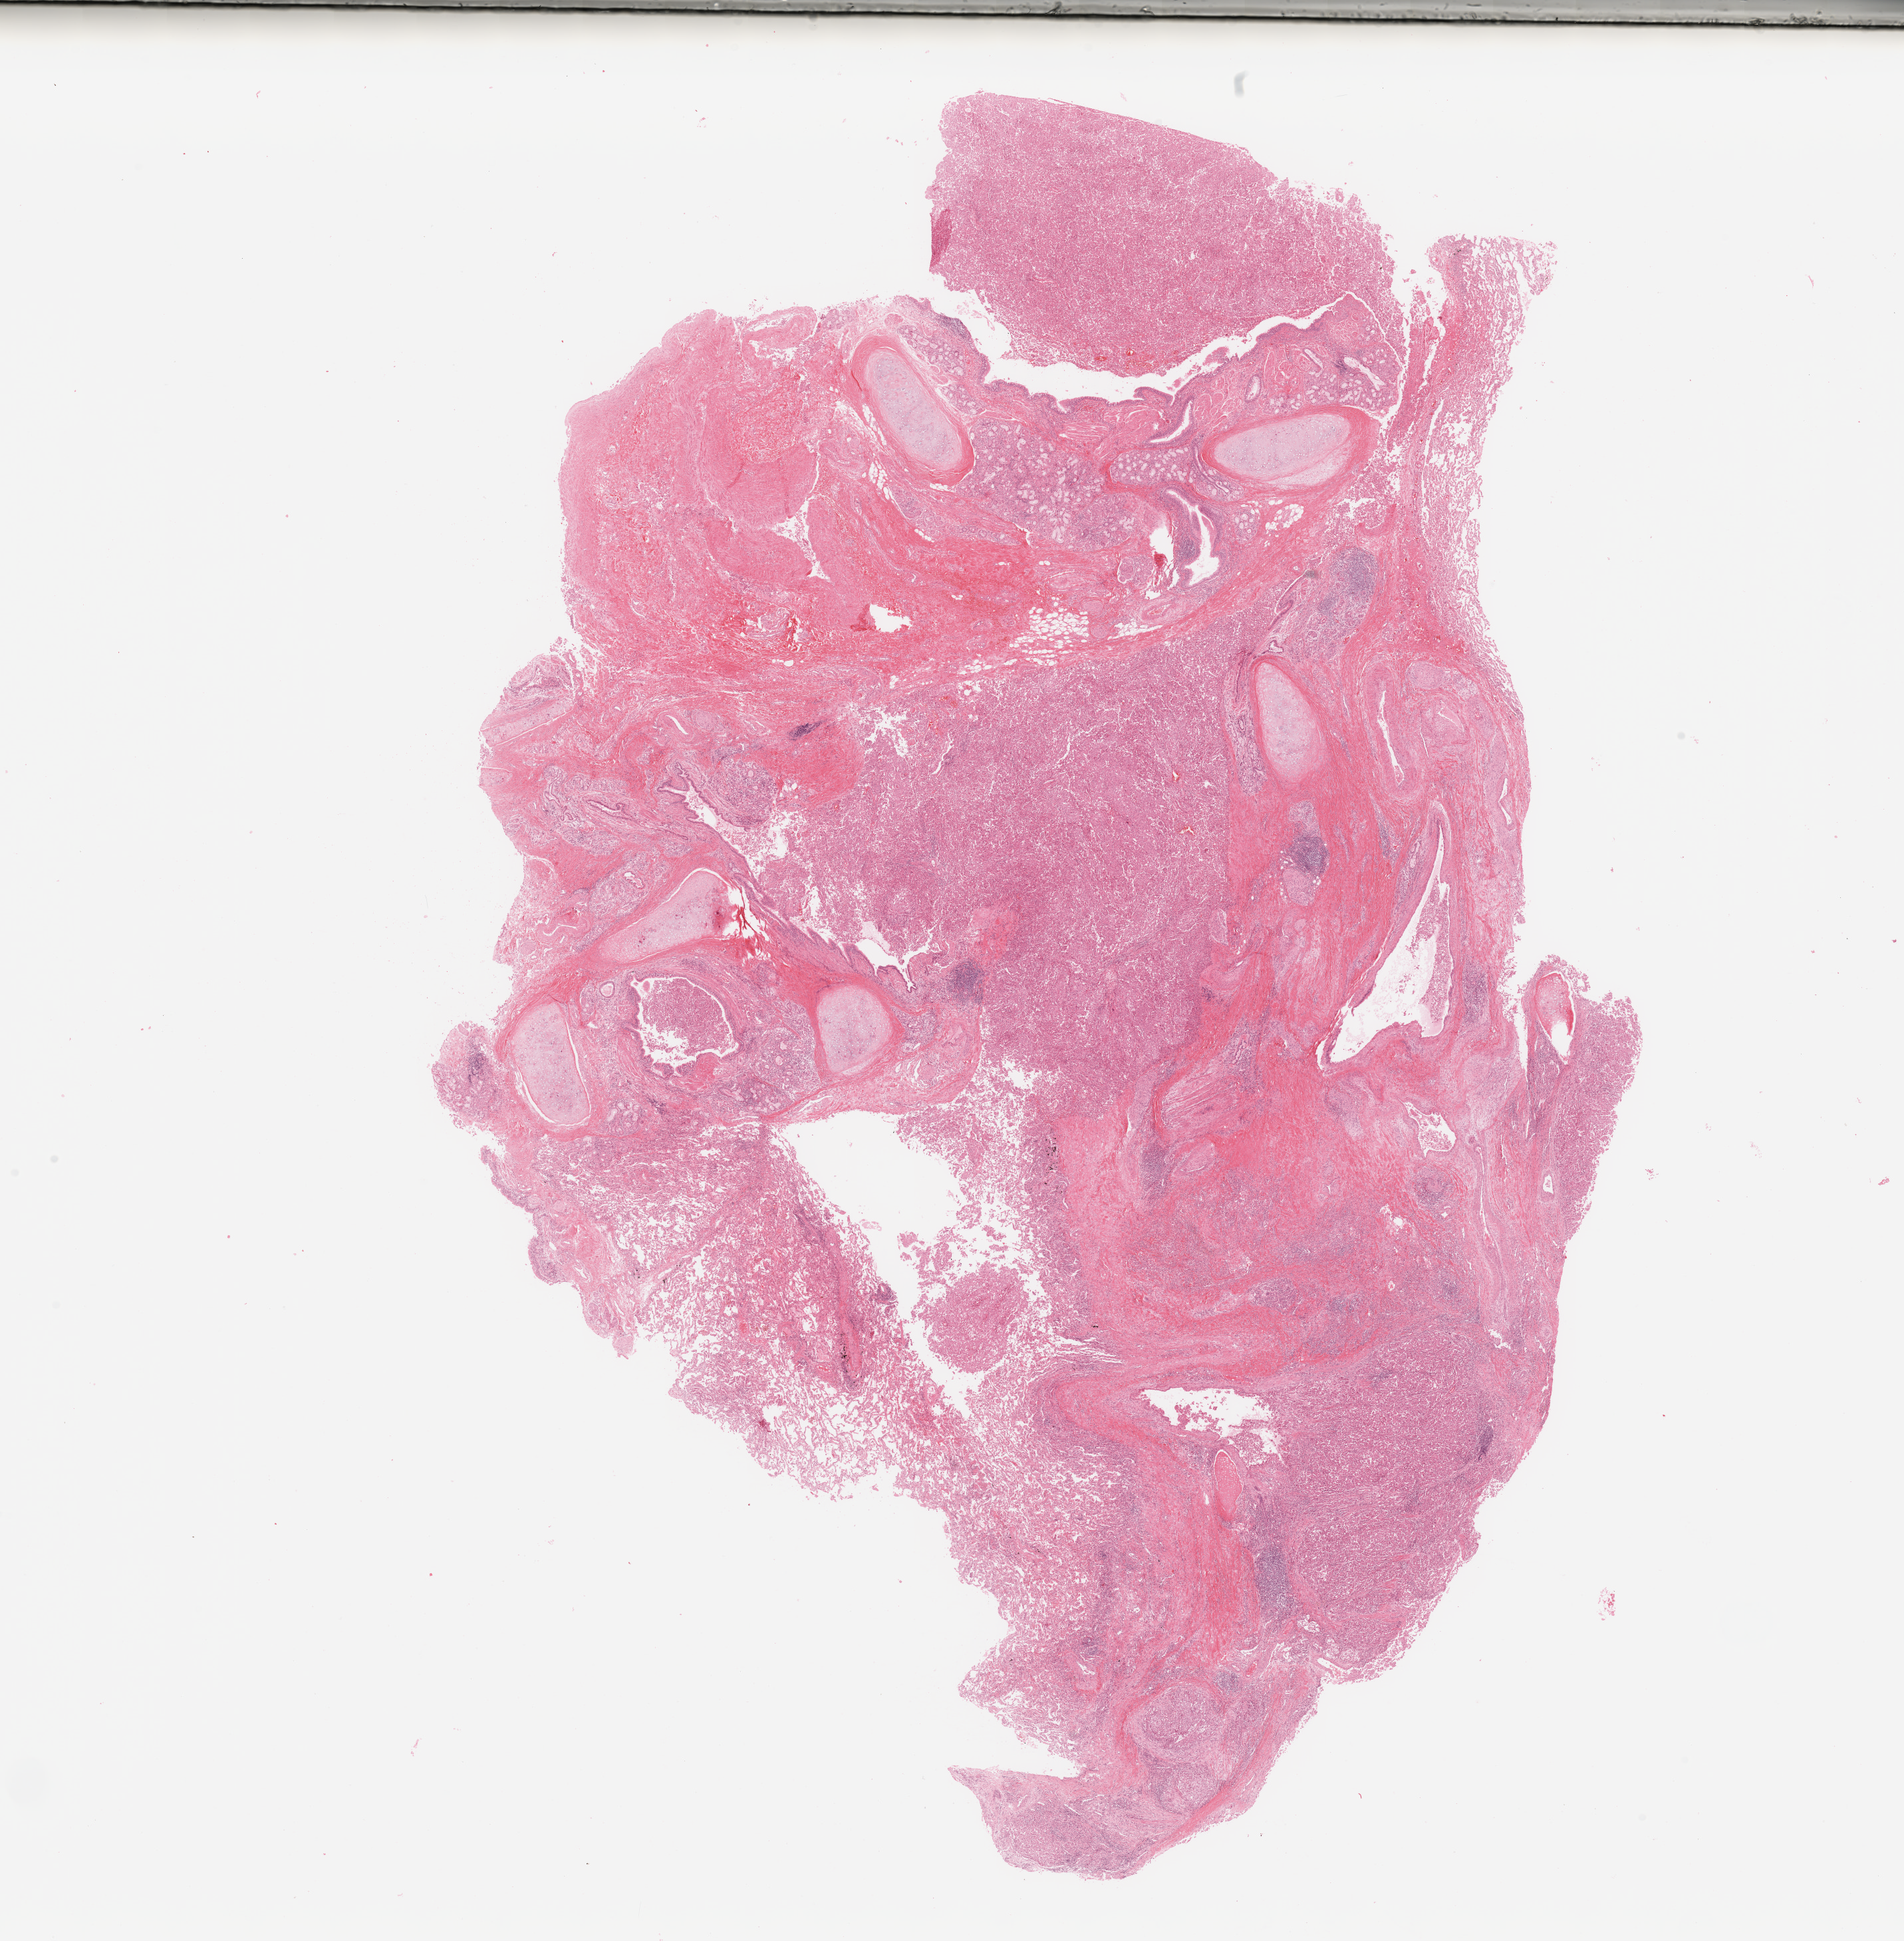
Whole-slide histology image, Hematoxylin and eosin (H&E) stained, whole scanned area (about 22.6 x 23.1 mm, slide scanned at 20x) shown as a low-resolution overview. Tumour tissue sample, lung. Patient: female, age 47 years.
Histologic diagnosis: Adenocarcinoma, NOS.